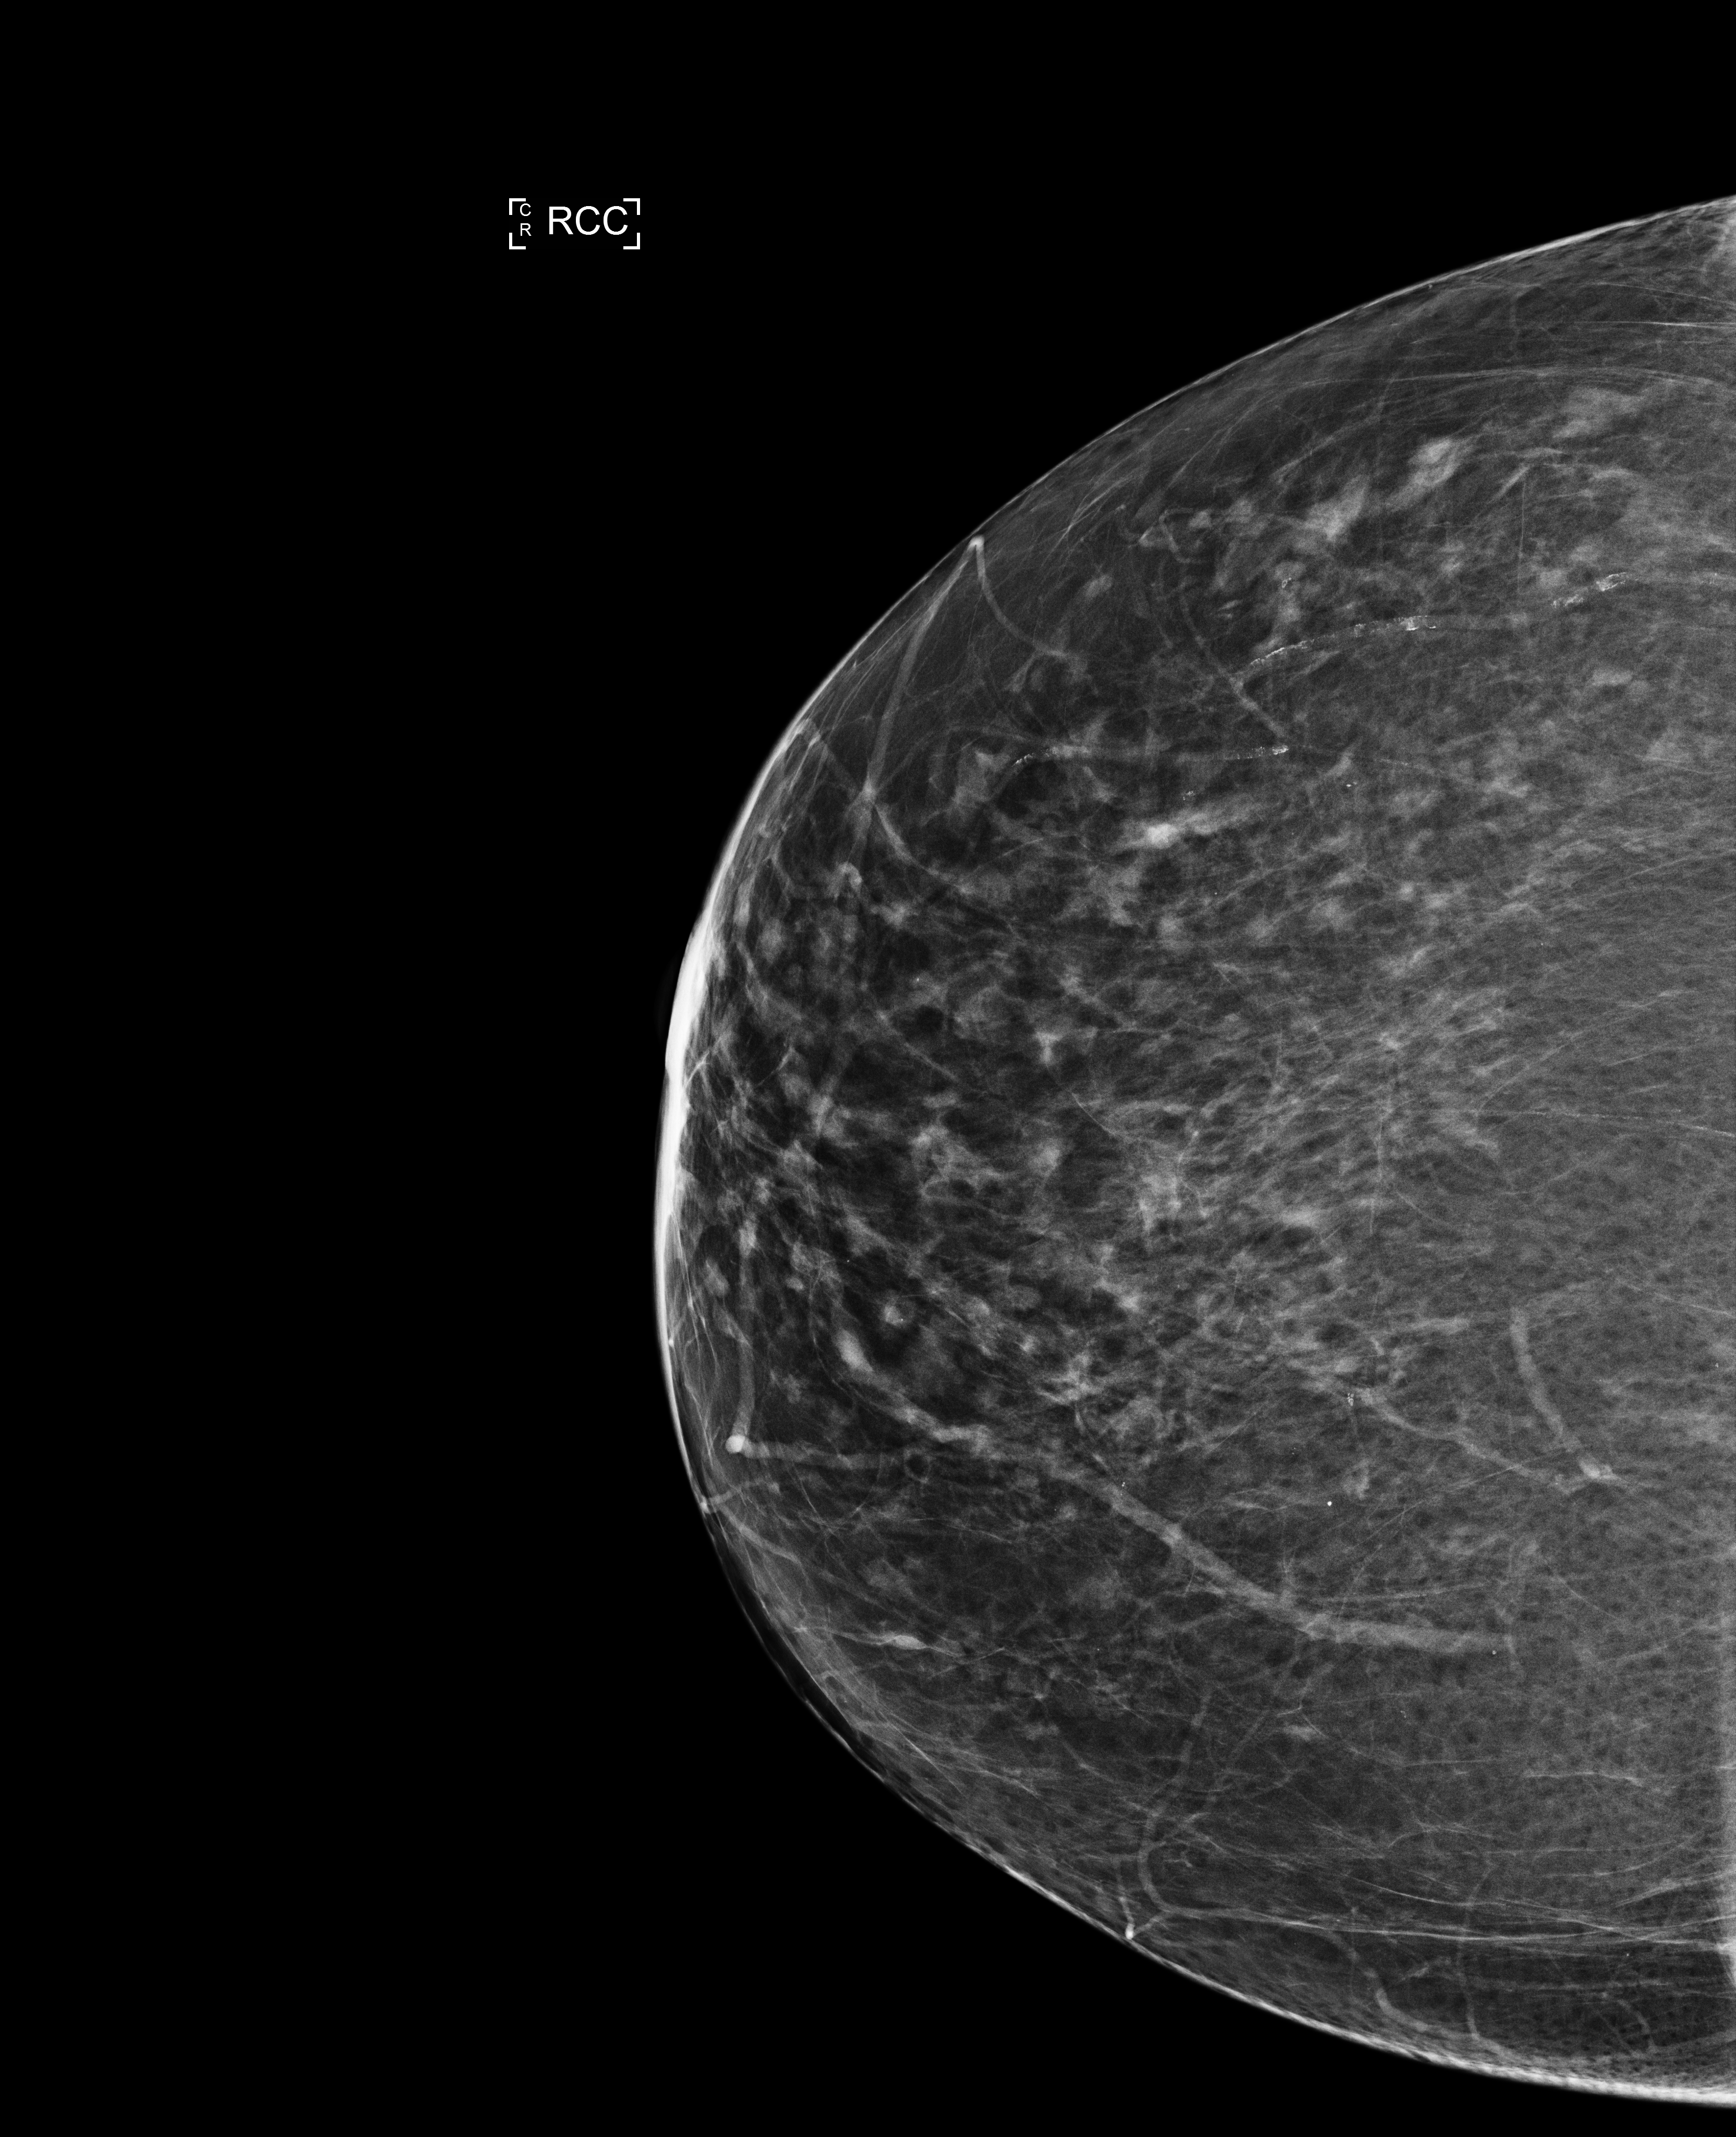
Screening examination, system: Selenia Dimensions. Patient: female, 74 years.
Image type: full-field digital mammogram. Breast: right. Projection: cranio-caudal projection.